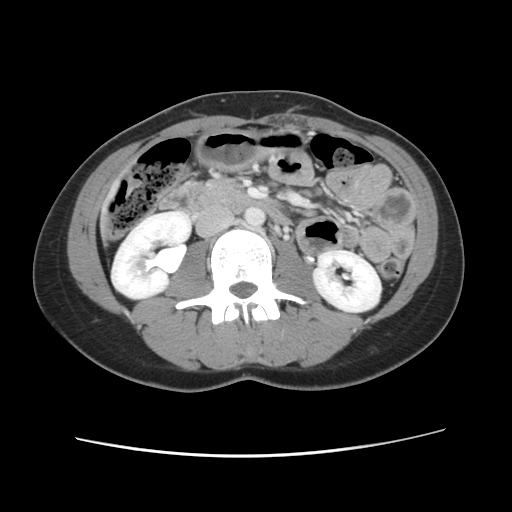
Contrast-enhanced abdominal CT, one axial slice; slice 20 of 134 in the series (ordered by position); intravenous contrast given; soft-tissue window (W 400 / L 40 HU); 2.5 mm slice thickness; 512 × 512 image matrix, field of view 339 × 339 mm. Female patient, age 33 years. From the clinical record (not read from this slice): diagnosis: colorectal cancer liver metastases, imaged before liver resection; multiple liver metastases: yes; largest metastasis: 4.5 cm; chemotherapy before resection: no.
Outlined on this slice (expert manual segmentation):
- liver: bounding box <108,191,116,209> (left, top, right, bottom; pixels)